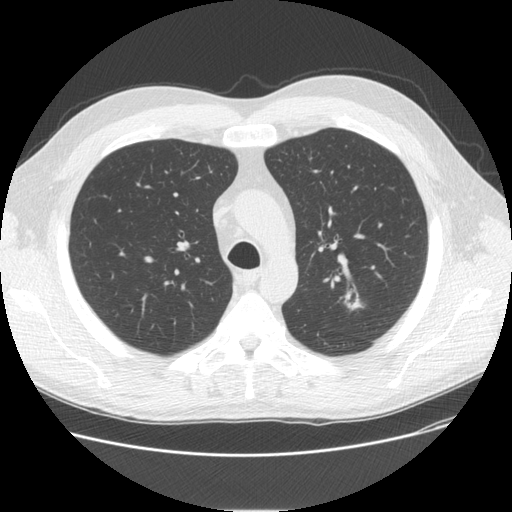
Chest CT (low-dose screening protocol), one axial image, third annual screen, lung window (W 1500 / L -600 HU), slice 38 of 150 in the series. Male participant, aged 57 years at enrolment. Current smoker at enrolment.
• Lesion marked by an expert reader, bounding box (x1, y1, x2, y2) in pixels: (323, 283, 374, 321).
• Reader record for this screening exam (exam-level; its link to the box is not recorded): non-calcified nodule or mass ≥4 mm, left upper lobe, 17 × 13 mm, spiculated (stellate) margins, mixed attenuation, pre-existing on the prior screen: yes; interval growth: yes.
• Official screen result: positive, other.
• Later outcome: lung cancer diagnosed 64 days after this screen — adenosquamous carcinoma, left upper lobe, poorly differentiated (G3), stage IA (AJCC 6th edition), 15 mm at pathology.